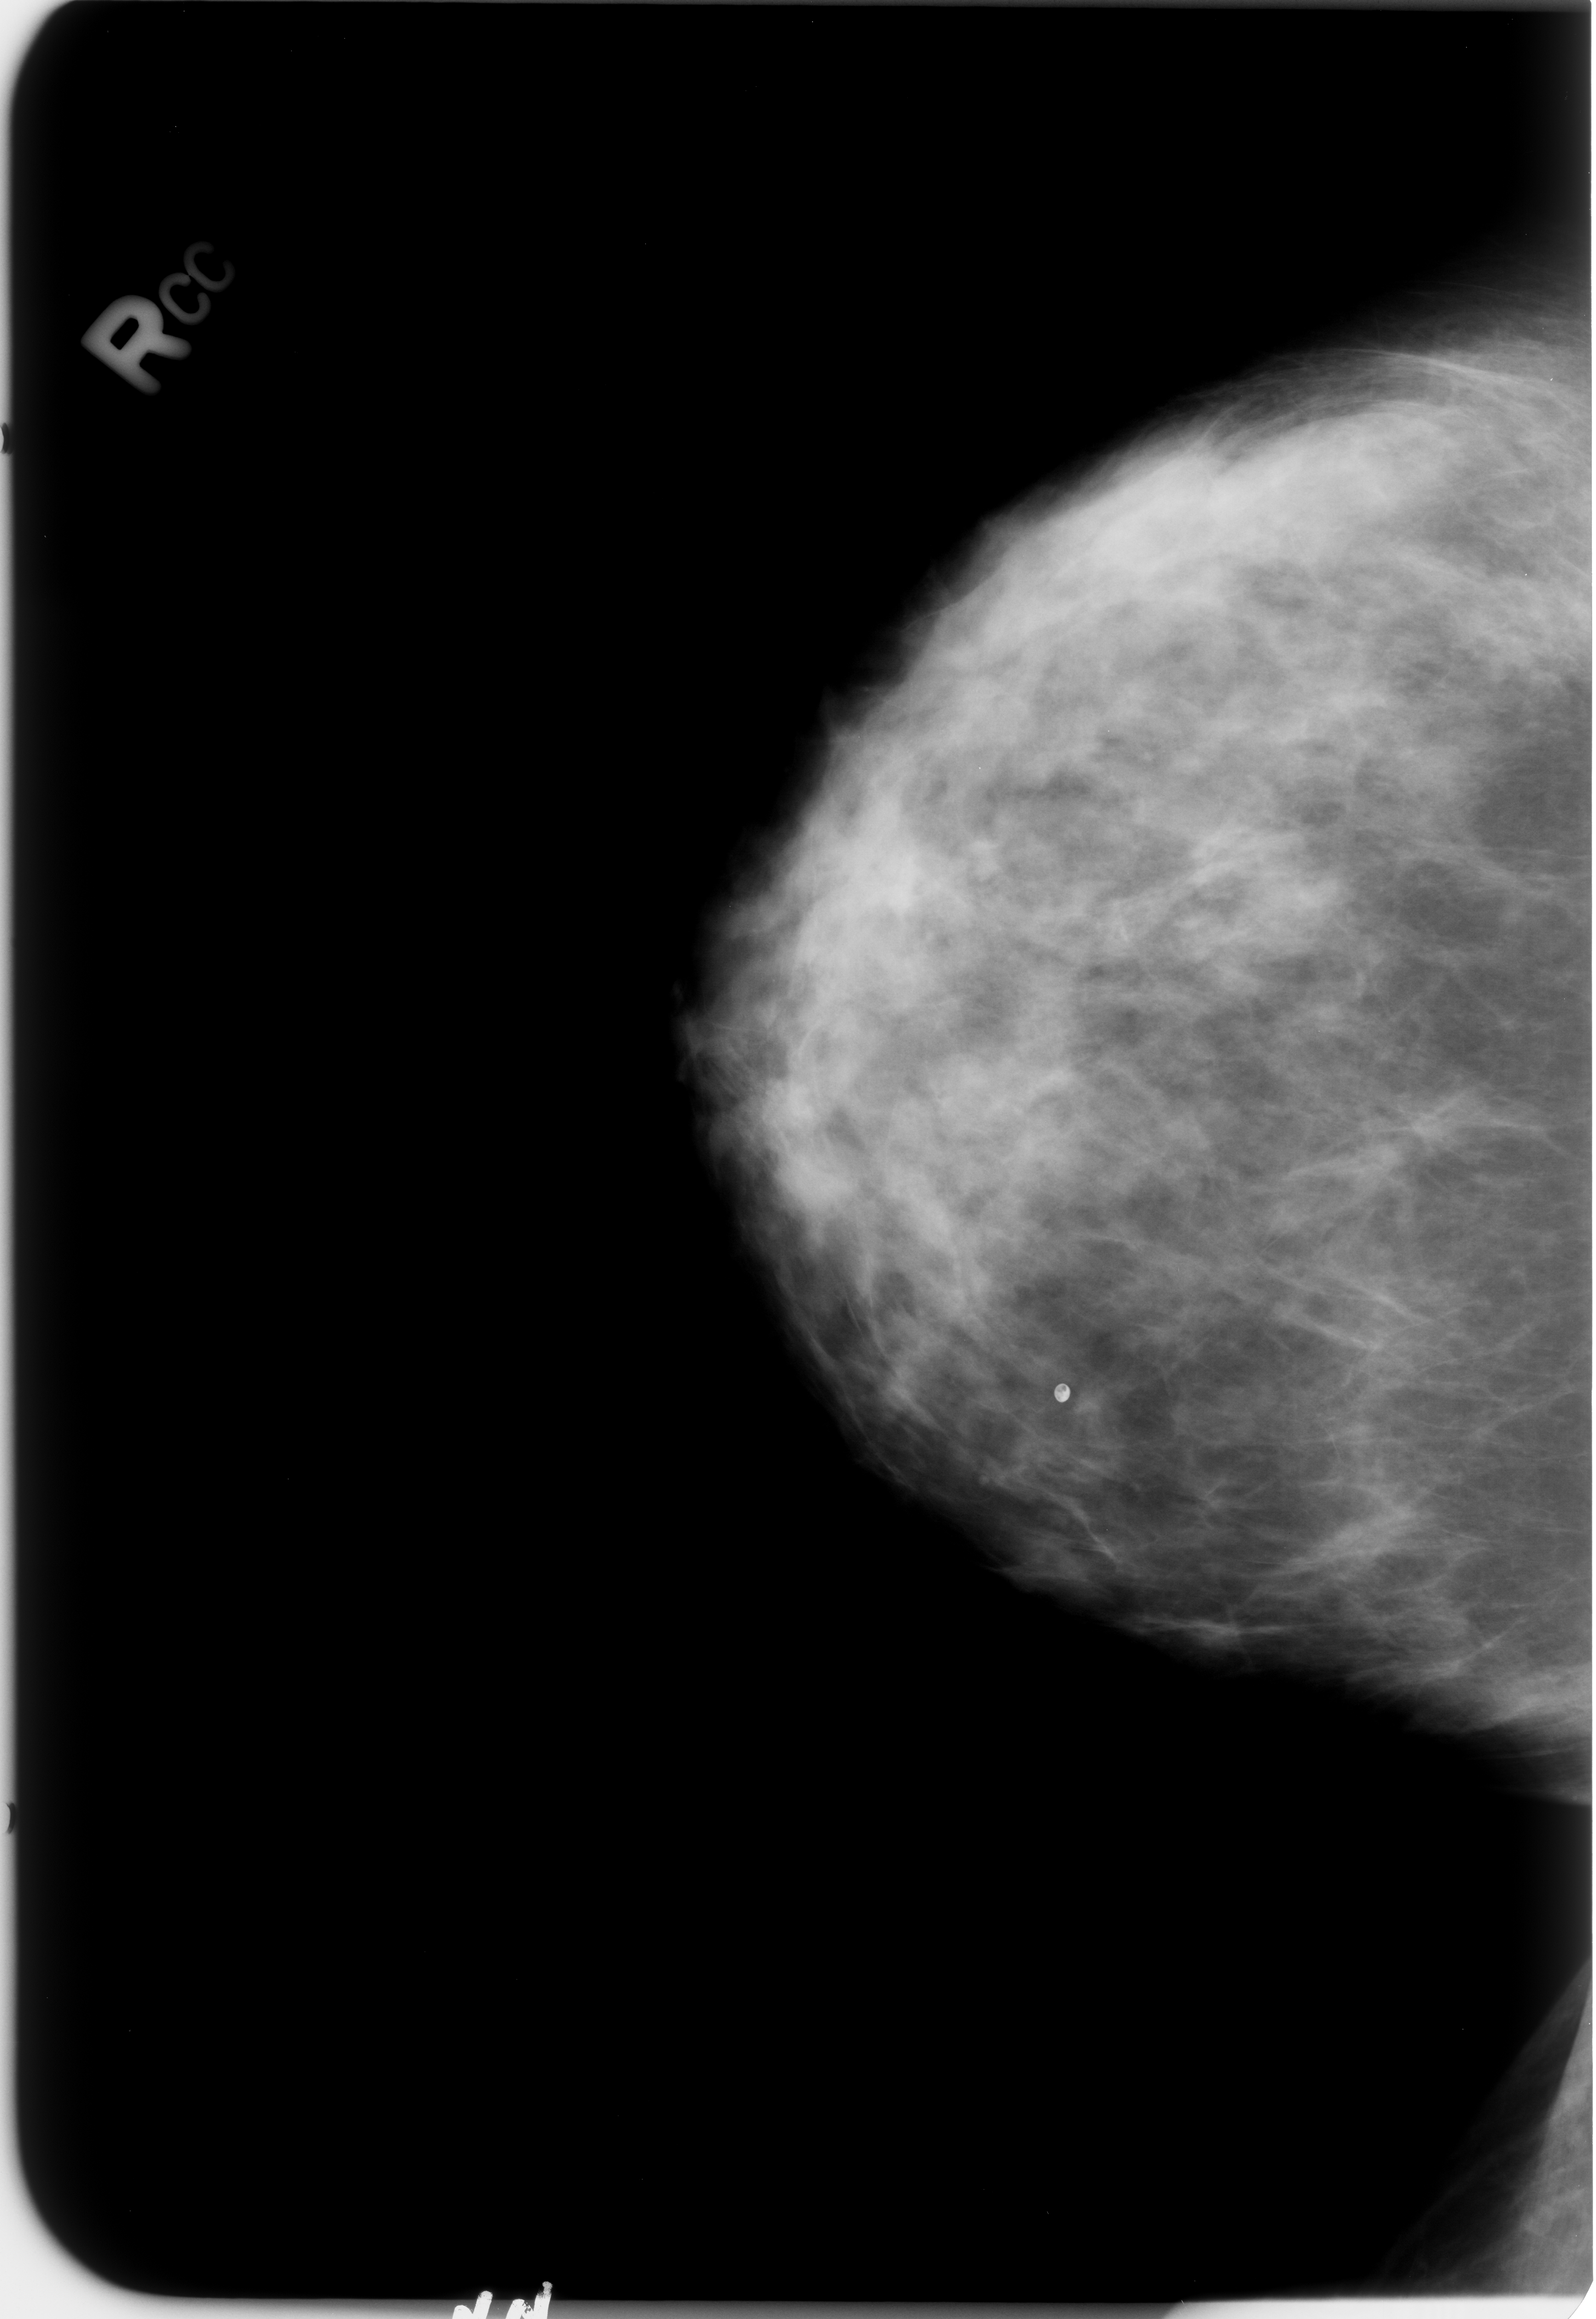
Scanned film-screen mammogram, right breast, craniocaudal (CC) view.
- Finding: mass, shape oval, margins circumscribed / obscured; BI-RADS assessment category 3; subtlety rating 3 on a 1 (subtle) to 5 (obvious) scale; pathology result (as recorded, not read from the image): benign.